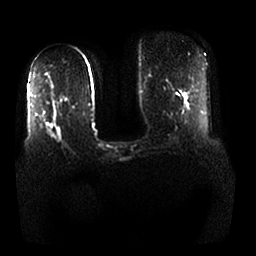
Breast MRI, one axial slice; position 14 of 25 along the scan axis; diffusion-weighted series; image 2 of 4 stored at this slice position (different b-values; order by instance number); 1.5 T; 256 × 256 image matrix. Female patient.
Annotated regions visible in this slice (outlined manually by an expert reader):
- tumour on diffusion-weighted imaging: box from (x=58, y=132) to (x=61, y=142) px